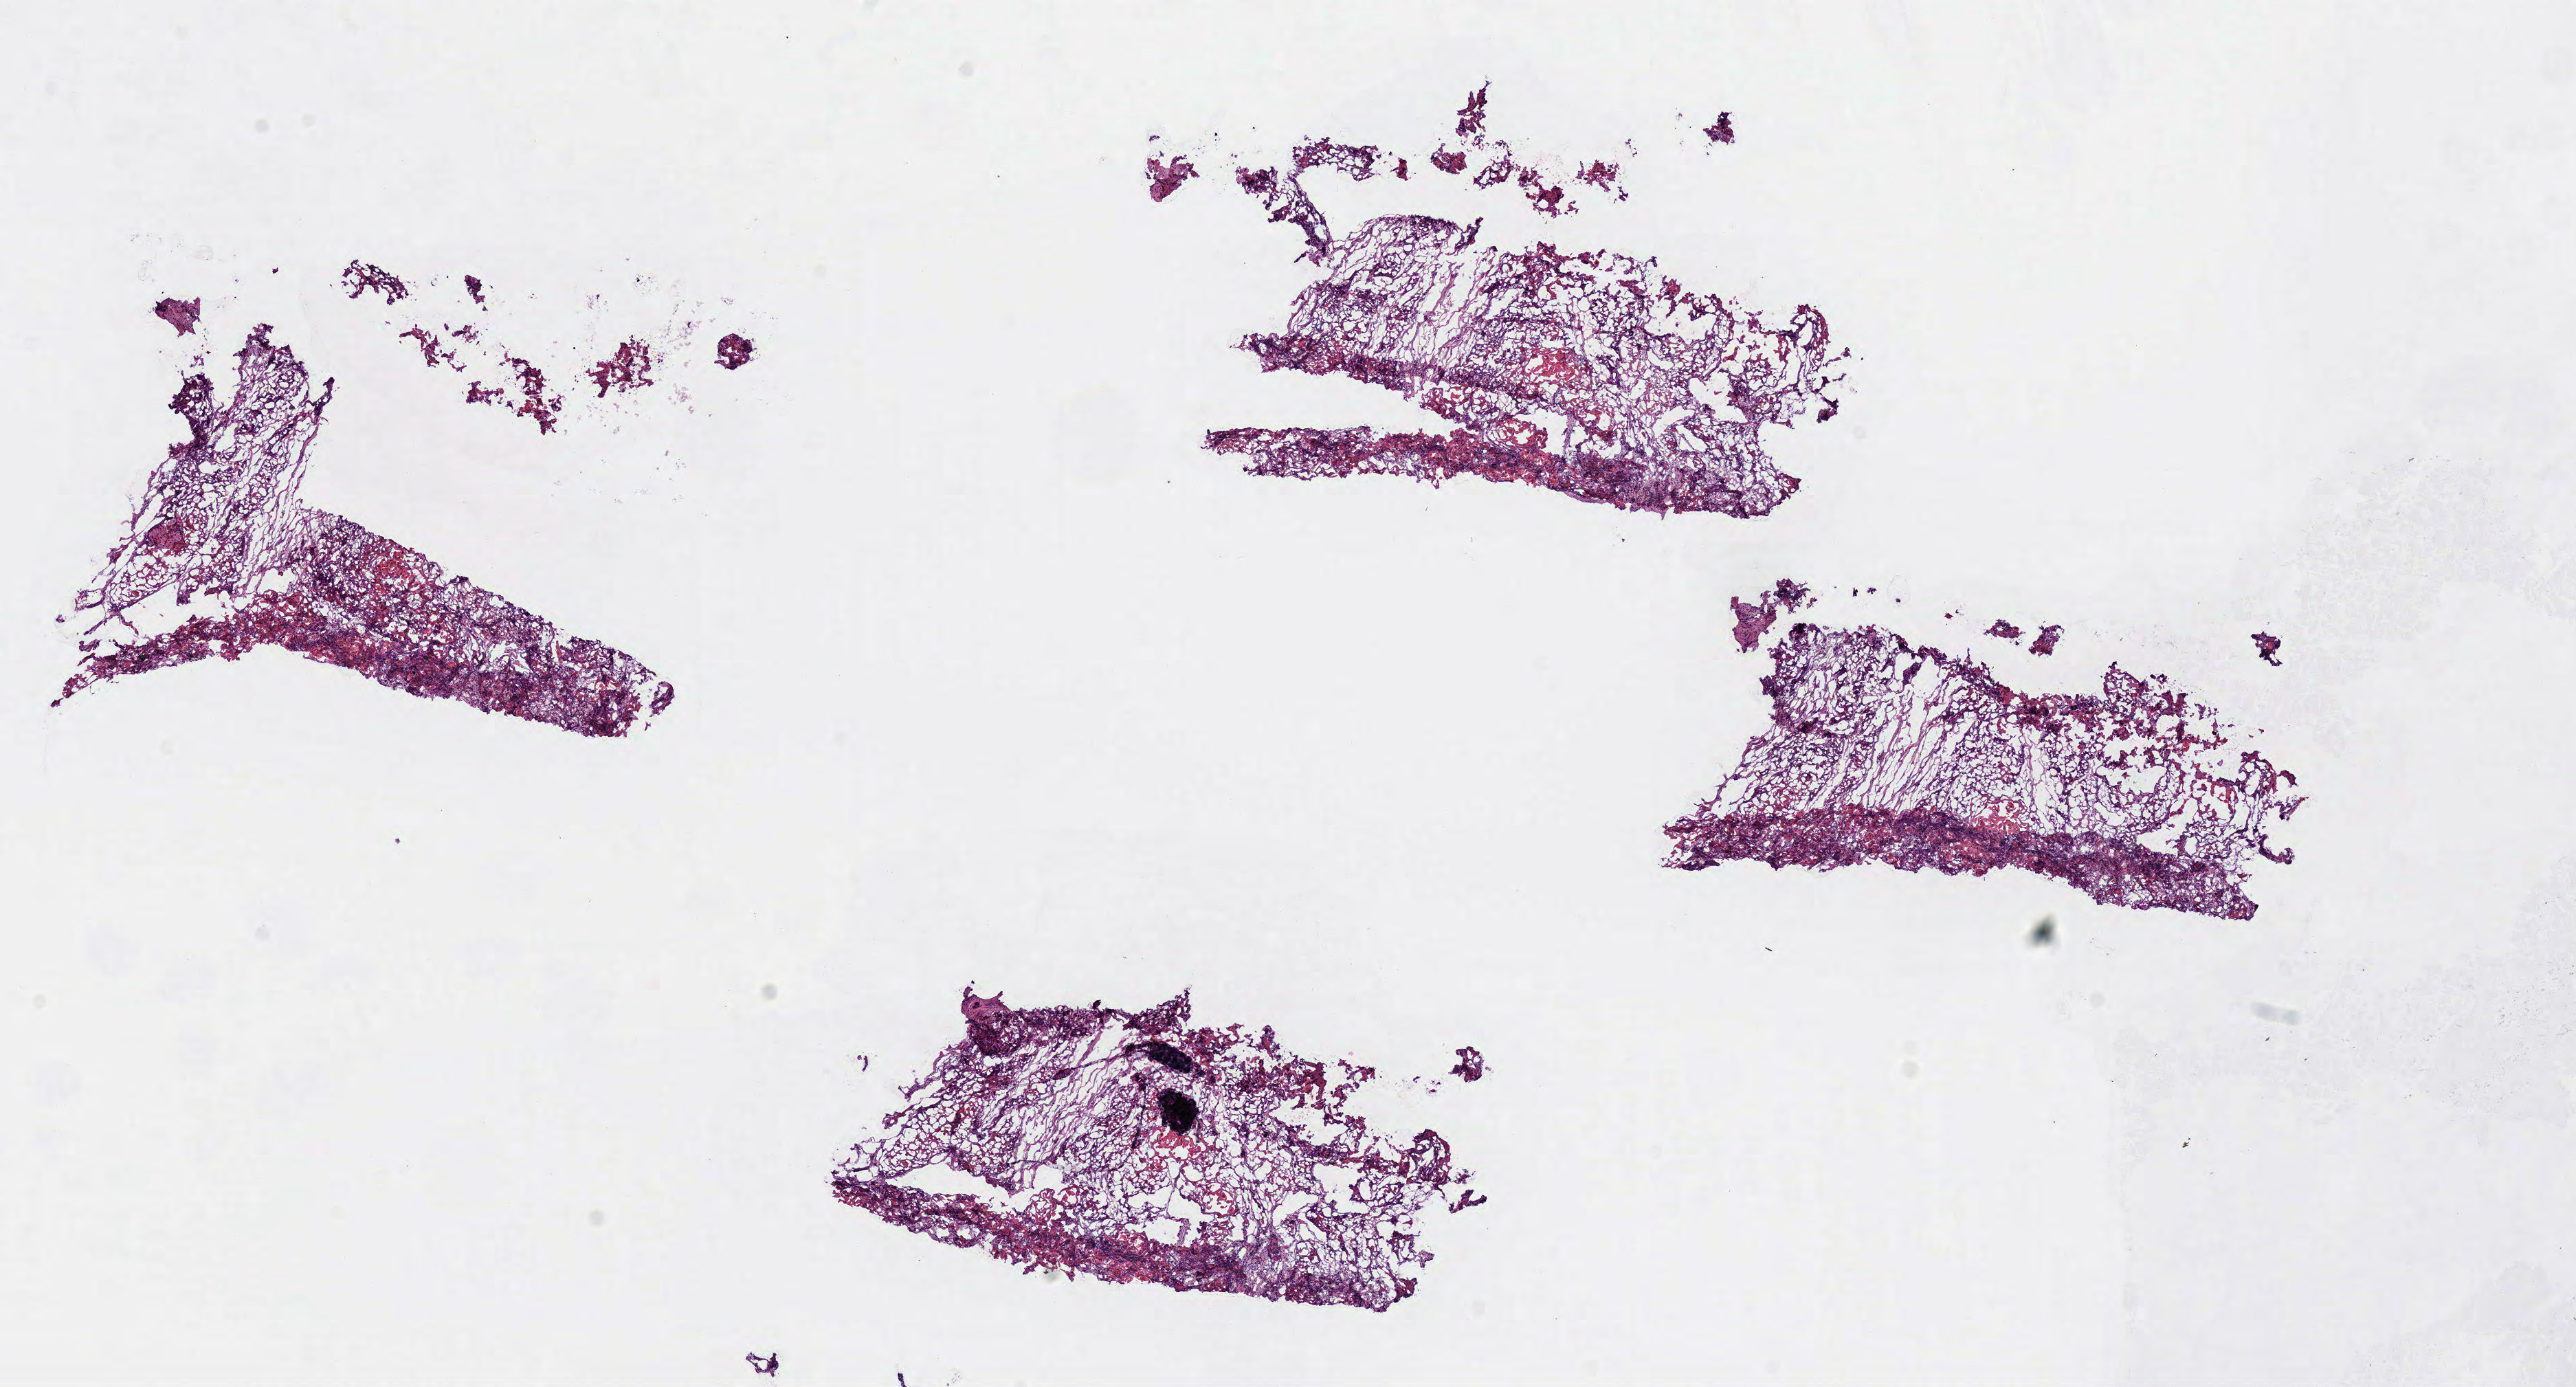
Whole-slide histology image, H&E — shown as a low-resolution overview of the whole scanned area (about 14.8 x 8.0 mm, acquisition: 40x scan); frozen section from the top of the tissue portion; head and neck, primary tumour sample. Patient: male, age at initial diagnosis 66 years. Histologic grade: G2 (moderately differentiated). Pathologist review of this section (percent, as recorded): tumour cells 75%, tumour nuclei 75%, normal cells 0%, stromal cells 25%, necrosis 0%.
* AJCC pathologic stage: IVA (7th edition)
* pathologic diagnosis: Squamous cell carcinoma, NOS (tongue, NOS)